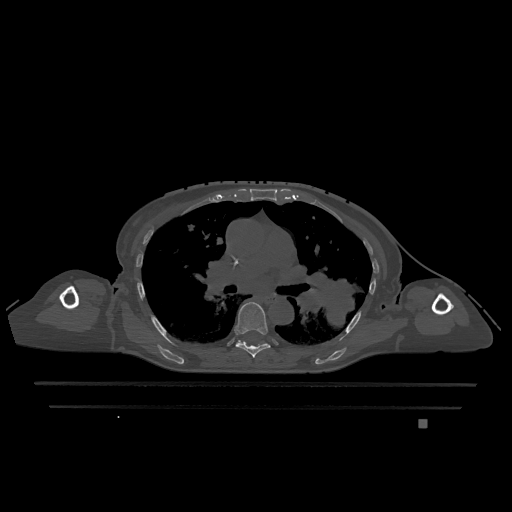
CT including the spine, one axial slice. Slice 782 of 1317 in the series (ordered by position). Bone window (W 1800 / L 400 HU). 0.5 mm slice thickness. 512 × 512 image matrix, field of view 500 × 500 mm. Patient: female, 74 years. From the clinical record (not read from this slice): primary cancer: lung.
Annotated regions visible in this slice (semi-automatically segmented with operator editing):
- T6 vertebra: bounding box [x1, y1, x2, y2] px = [235, 302, 270, 358]